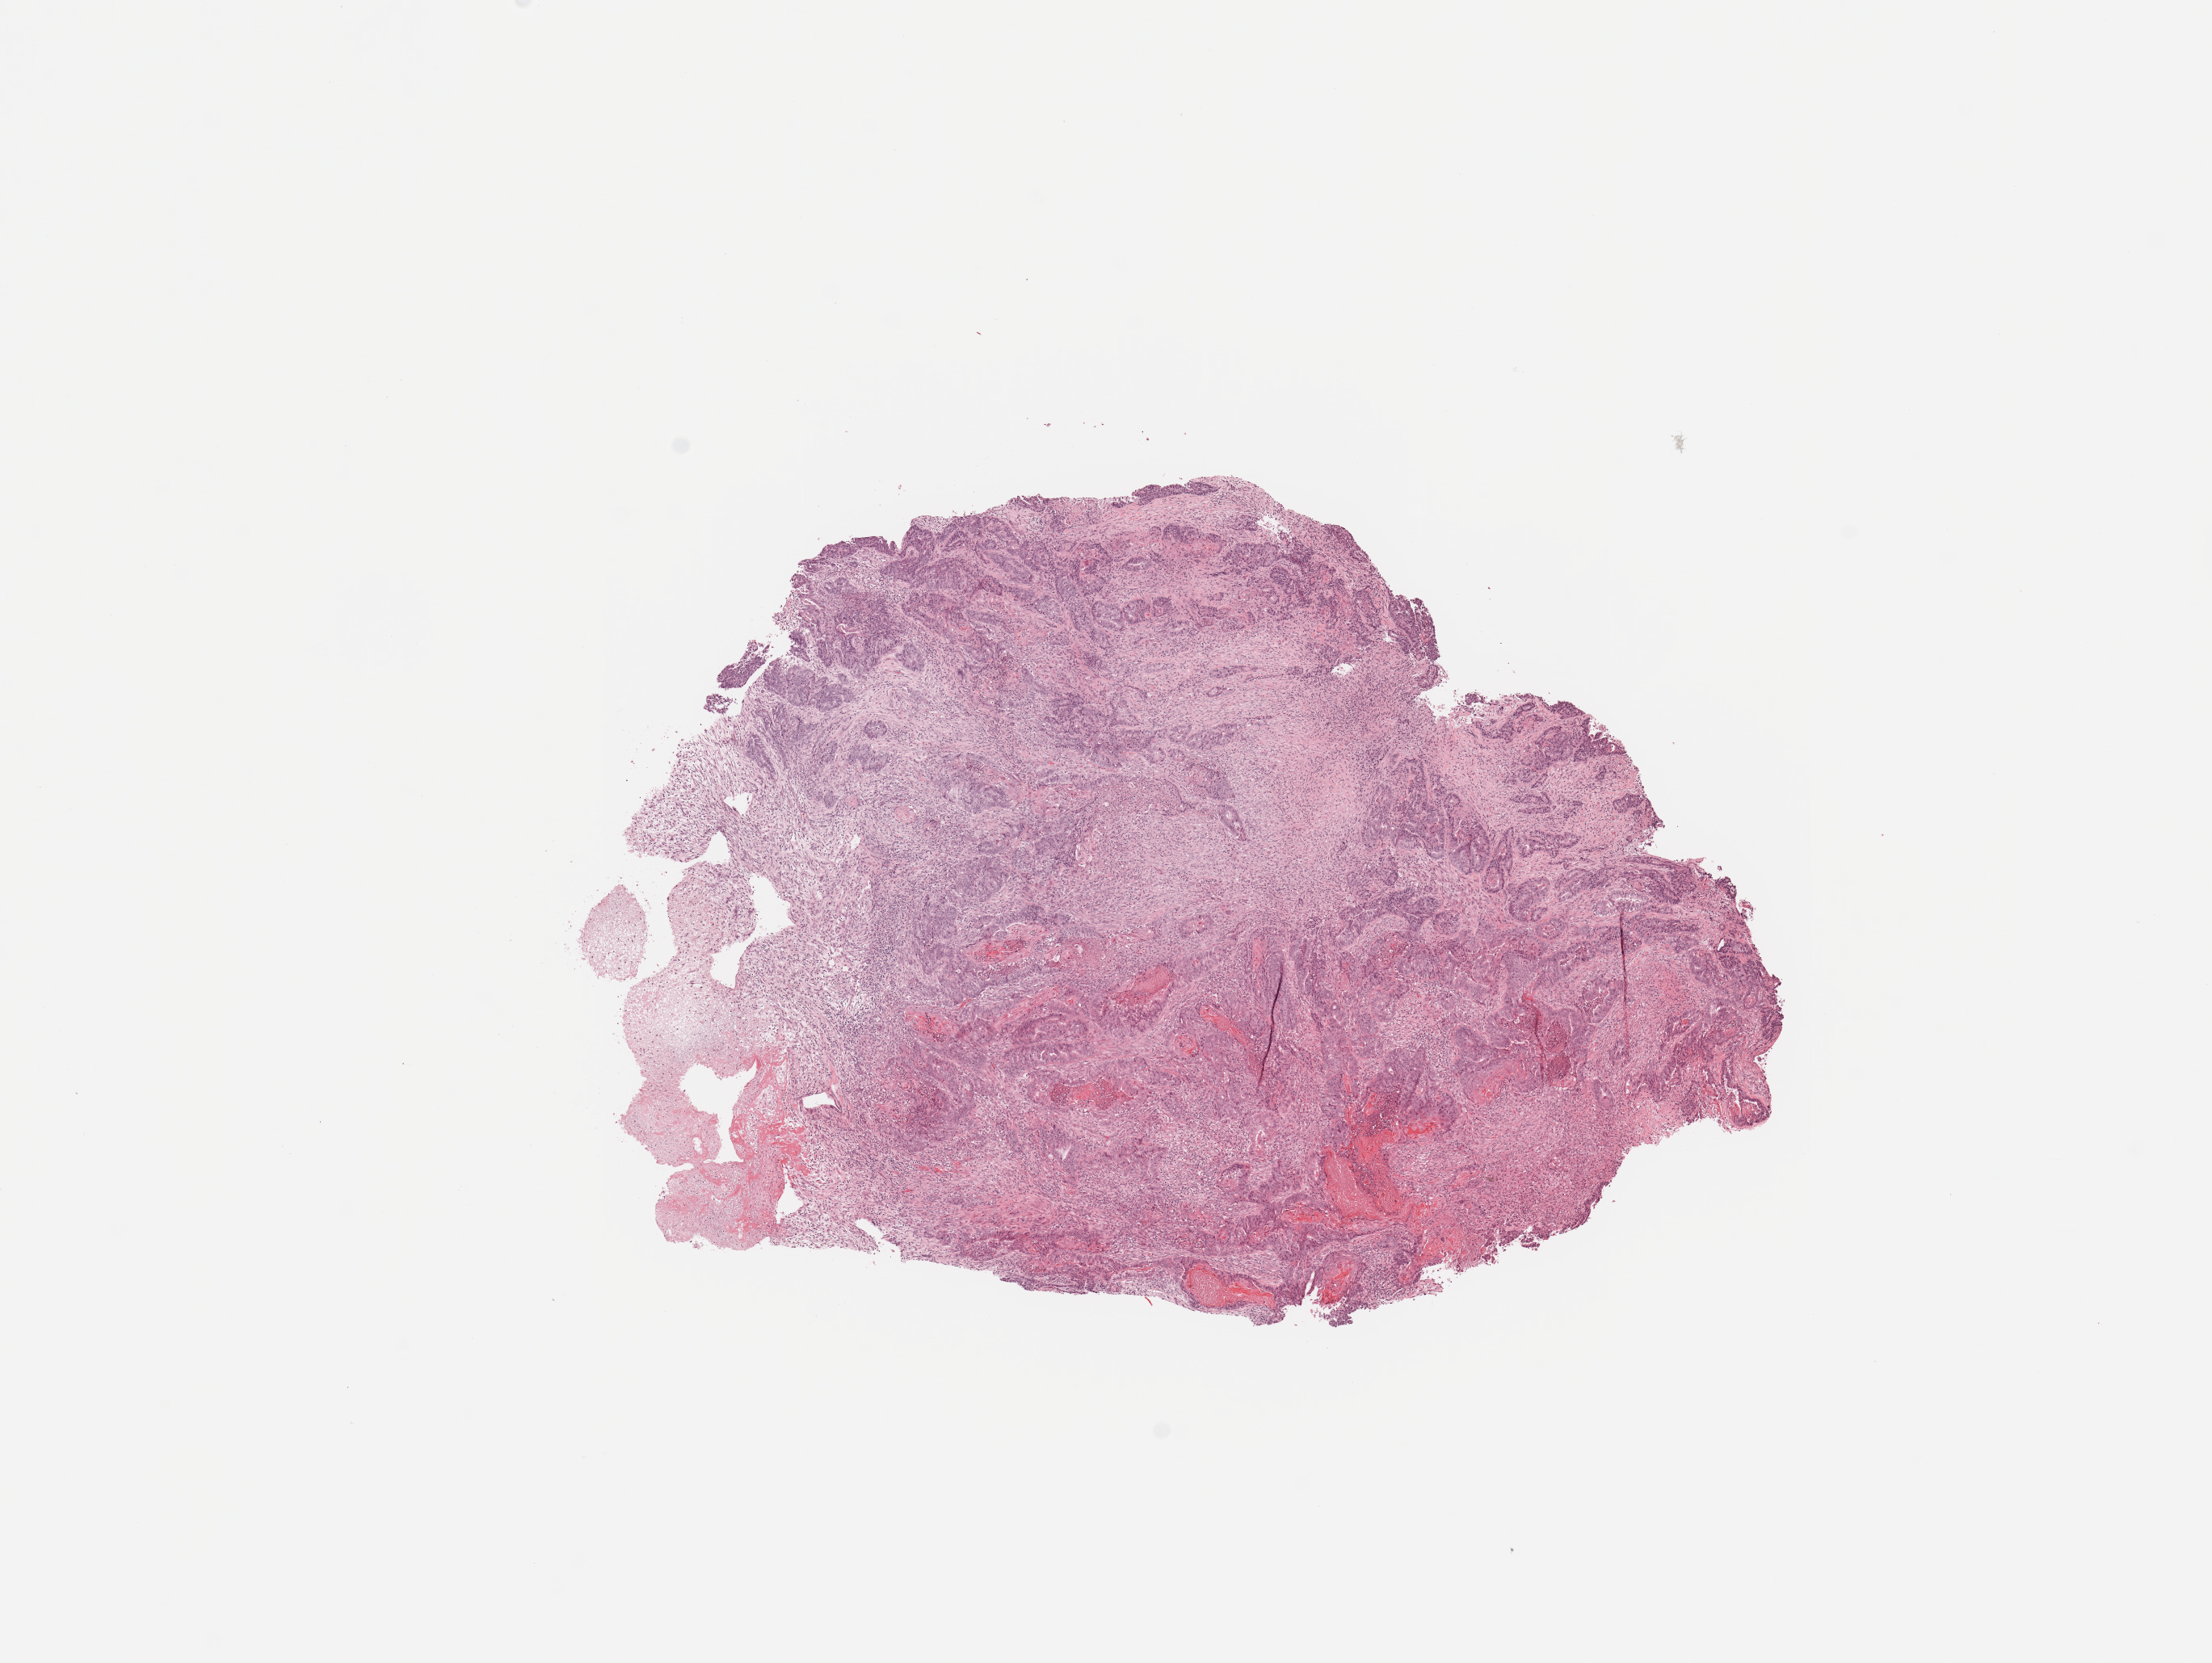
Hematoxylin and eosin (H&E) stained whole-slide image, low-resolution overview of the scanned area, about 10.8 x 8.1 mm; tumour tissue sample, uterus. 72-year-old female patient.
Patient diagnosis (cohort enrolment): corpus endometrial carcinoma (uterus).